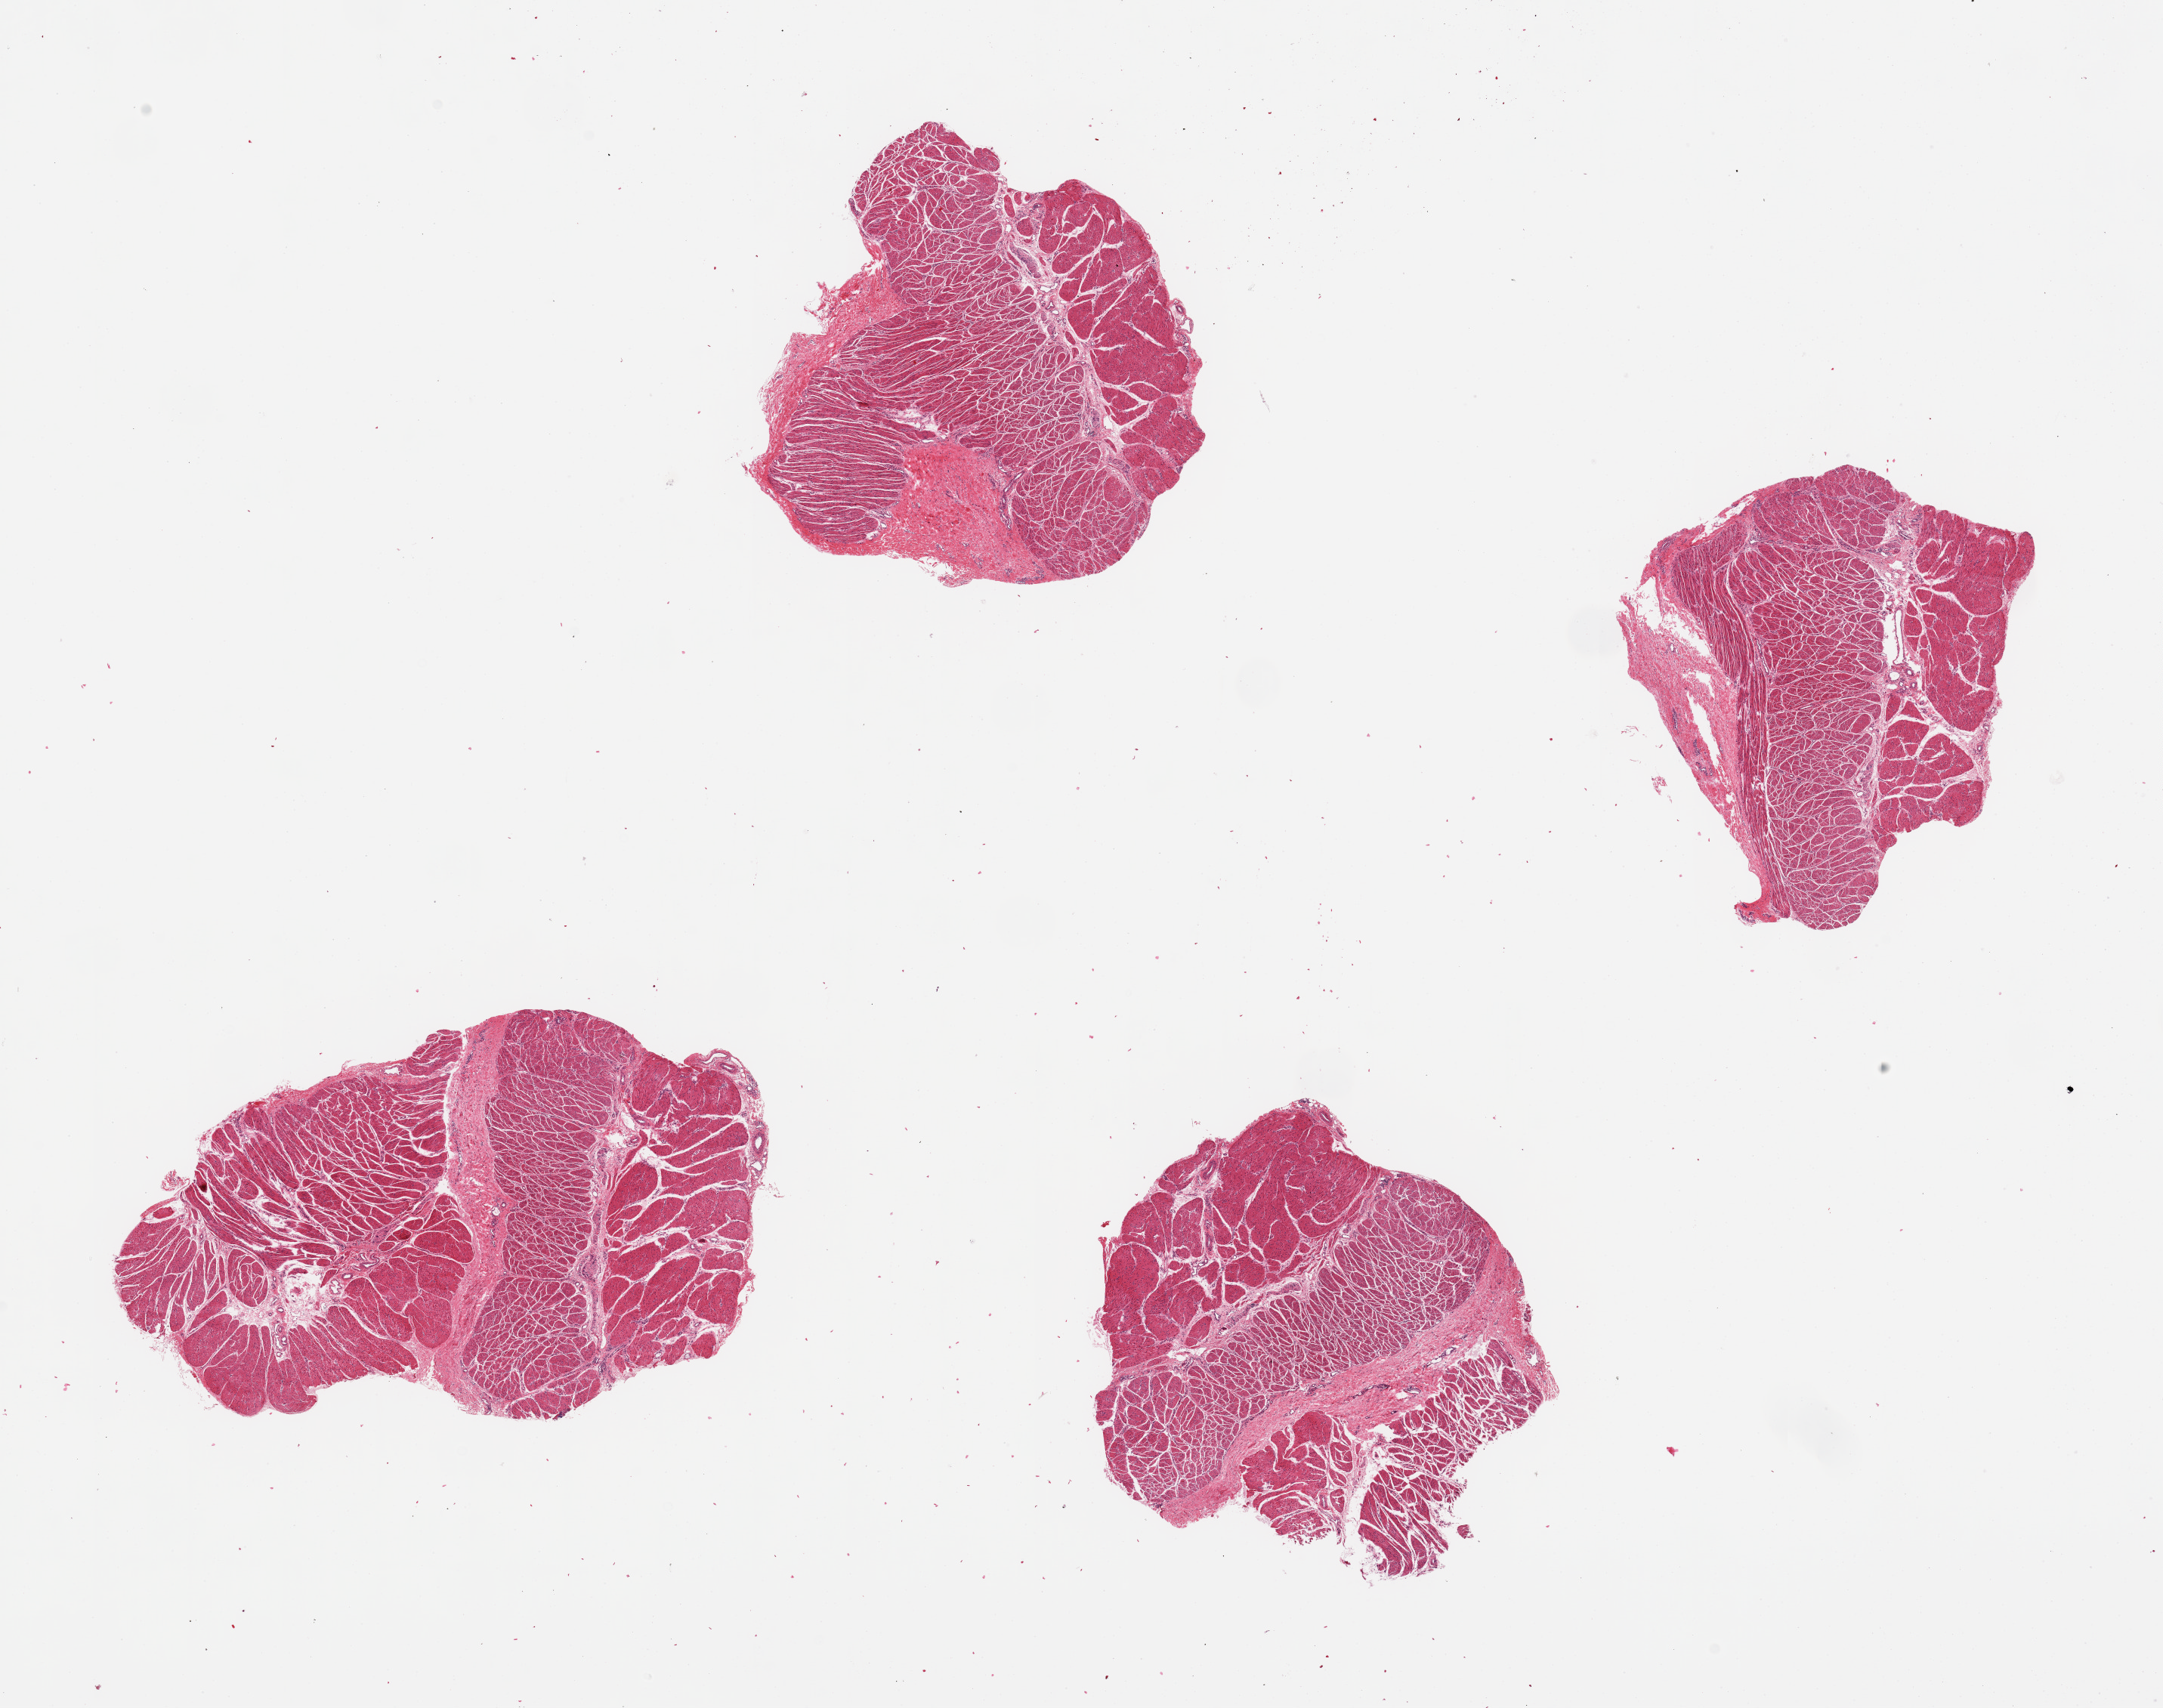
Whole-slide image, haematoxylin and eosin stain — a low-resolution overview of the entire scanned area, about 22.6 x 17.9 mm; PAXgene-fixed, paraffin-embedded tissue; sampled site (target tissue): gastroesophageal junction; tissue donor sample. Donor sex: male.
Pathologist's review note for this sample: 4 pieces; well dissected.